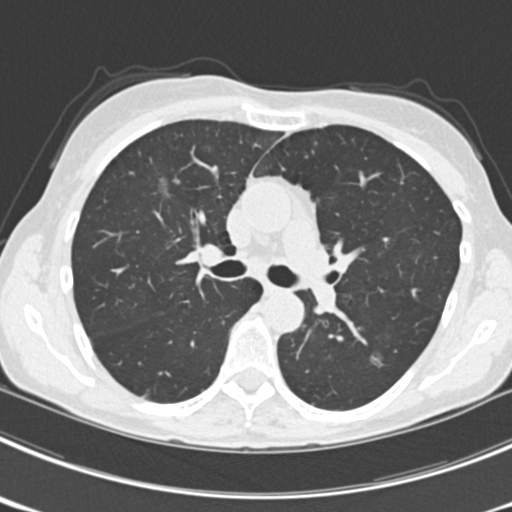
Axial slice from a low-dose chest CT screening exam. Third screening round (two years after baseline). Lung window (W 1500 / L -600 HU). 2 mm slice thickness. Slice 80 of 225 in the series. 512 × 512 image matrix. Female participant, aged 63 years at enrolment. Current smoker at enrolment.
Lesion marked by an expert reader, box from (x=357, y=339) to (x=397, y=381) px. The screening reader recorded 9 non-calcified nodules or masses ≥4 mm on this exam (left upper lobe, right upper lobe, left upper lobe, left lower lobe, right middle lobe, left lower lobe, left lower lobe, right lower lobe, right lower lobe); which of them this box marks is not recorded. Official screen result: positive, other.